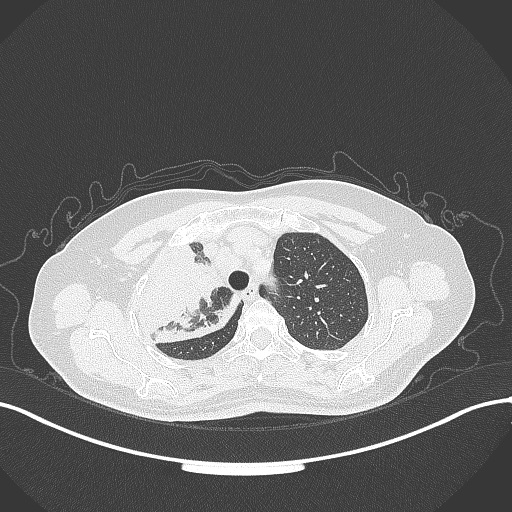
Chest CT, one axial slice. Position 250 of 309 along the scan axis. Reconstruction kernel B70f. 120 kVp. Lung window (W 1500 / L -600 HU). 1 mm slice thickness. 512 × 512 image matrix, field of view 400 × 400 mm. Female patient, age 60 years. Case-level facts recorded for this patient, not image findings: clinical TNM (as recorded): T3 N1 M1.
Structures marked on this image (rectangle marked by the reading radiologist):
- lung tumour (recorded histology: adenocarcinoma): box from (x=124, y=231) to (x=245, y=347) px